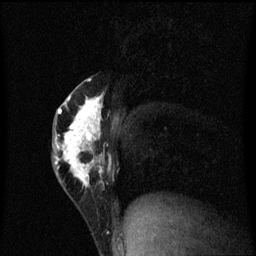
Breast MRI (dynamic contrast-enhanced), one sagittal slice; slice 30 of 60 in the series (ordered by position); dynamic contrast-enhanced series, image 2 of 3 at this slice position (ordered by acquisition); 1.5 T; TE 4.2 ms, TR 8.4 ms; 2 mm slice thickness; 256 × 256 image matrix, field of view 200 × 200 mm. Female patient, age 40 years.
Annotated regions visible in this slice (semi-automatic segmentation, software-assisted and operator-edited):
- analysis volume of interest (the breast-tissue region the enhancement analysis was run in; not a lesion): box from (x=53, y=76) to (x=112, y=203) px
- tumour enhancement mask (voxels above the 70 % enhancement threshold inside the analysis volume of interest): (x=54, y=78)–(x=112, y=187)